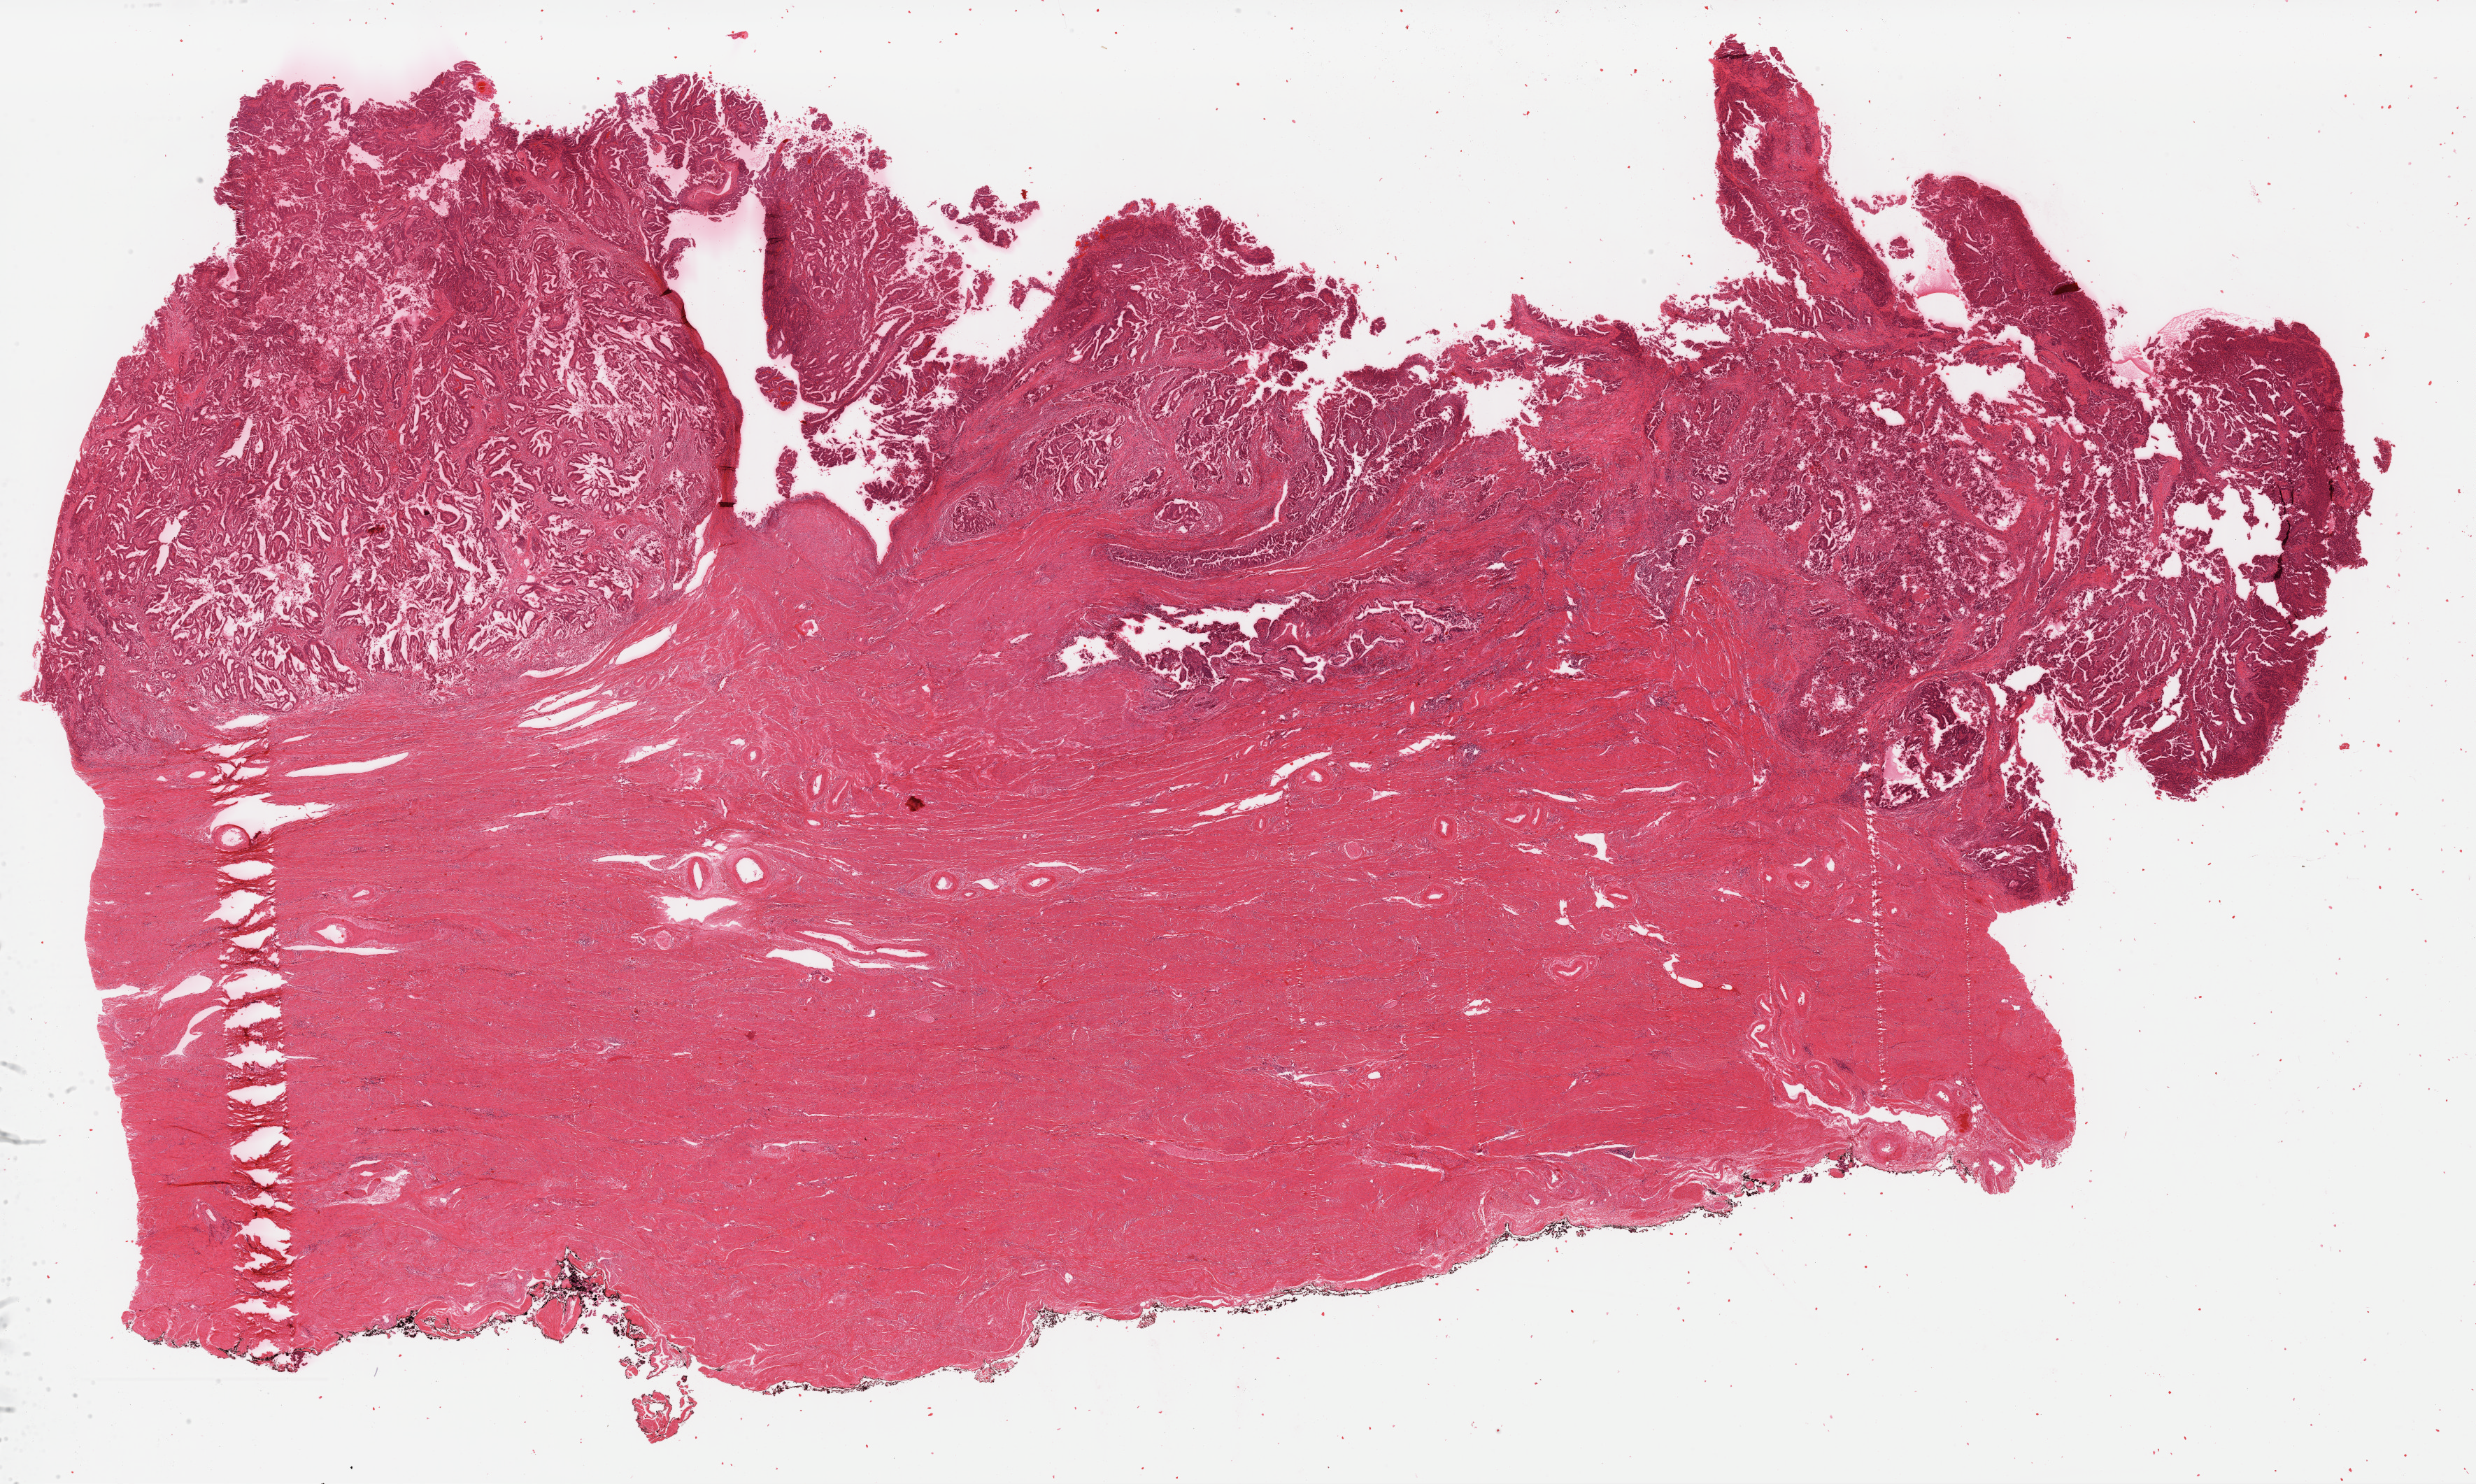
Hematoxylin and eosin (H&E) stained whole-slide image — shown as a low-resolution overview of the whole scanned area (about 28.0 x 16.8 mm). Formalin-fixed paraffin-embedded (FFPE) diagnostic section. Primary tumour sample from the uterus. Female patient; age at initial diagnosis 37 years. Histologic grade: G2 (moderately differentiated).
Lymph nodes positive (case pathology): 0 of 13 examined. FIGO stage: IIIA. Histologic diagnosis: Endometrioid adenocarcinoma, NOS (endometrium).